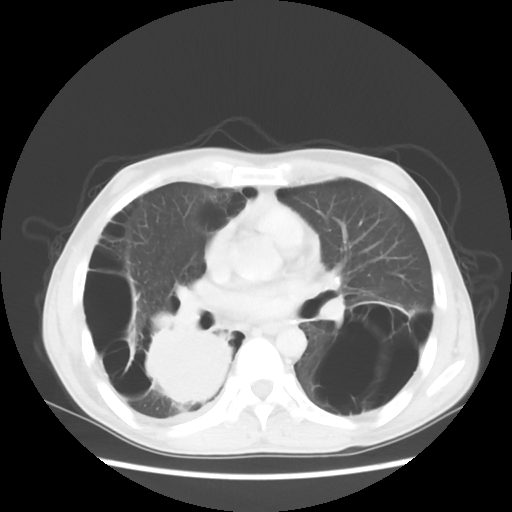
Chest CT, one axial slice. Reconstruction kernel STANDARD. Lung window (W 1500 / L -600 HU). 5 mm slice thickness. 512 × 512 image matrix, field of view 351 × 351 mm. Patient: male, 41 years. Case-level facts recorded for this patient, not image findings: clinical TNM (as recorded): T4 N0 M1a; histopathological grade: G3.
Annotated regions visible in this slice (bounding box drawn by a radiologist):
- lung tumour (recorded histology: large cell carcinoma): bounding box <137,322,243,410> (left, top, right, bottom; pixels)